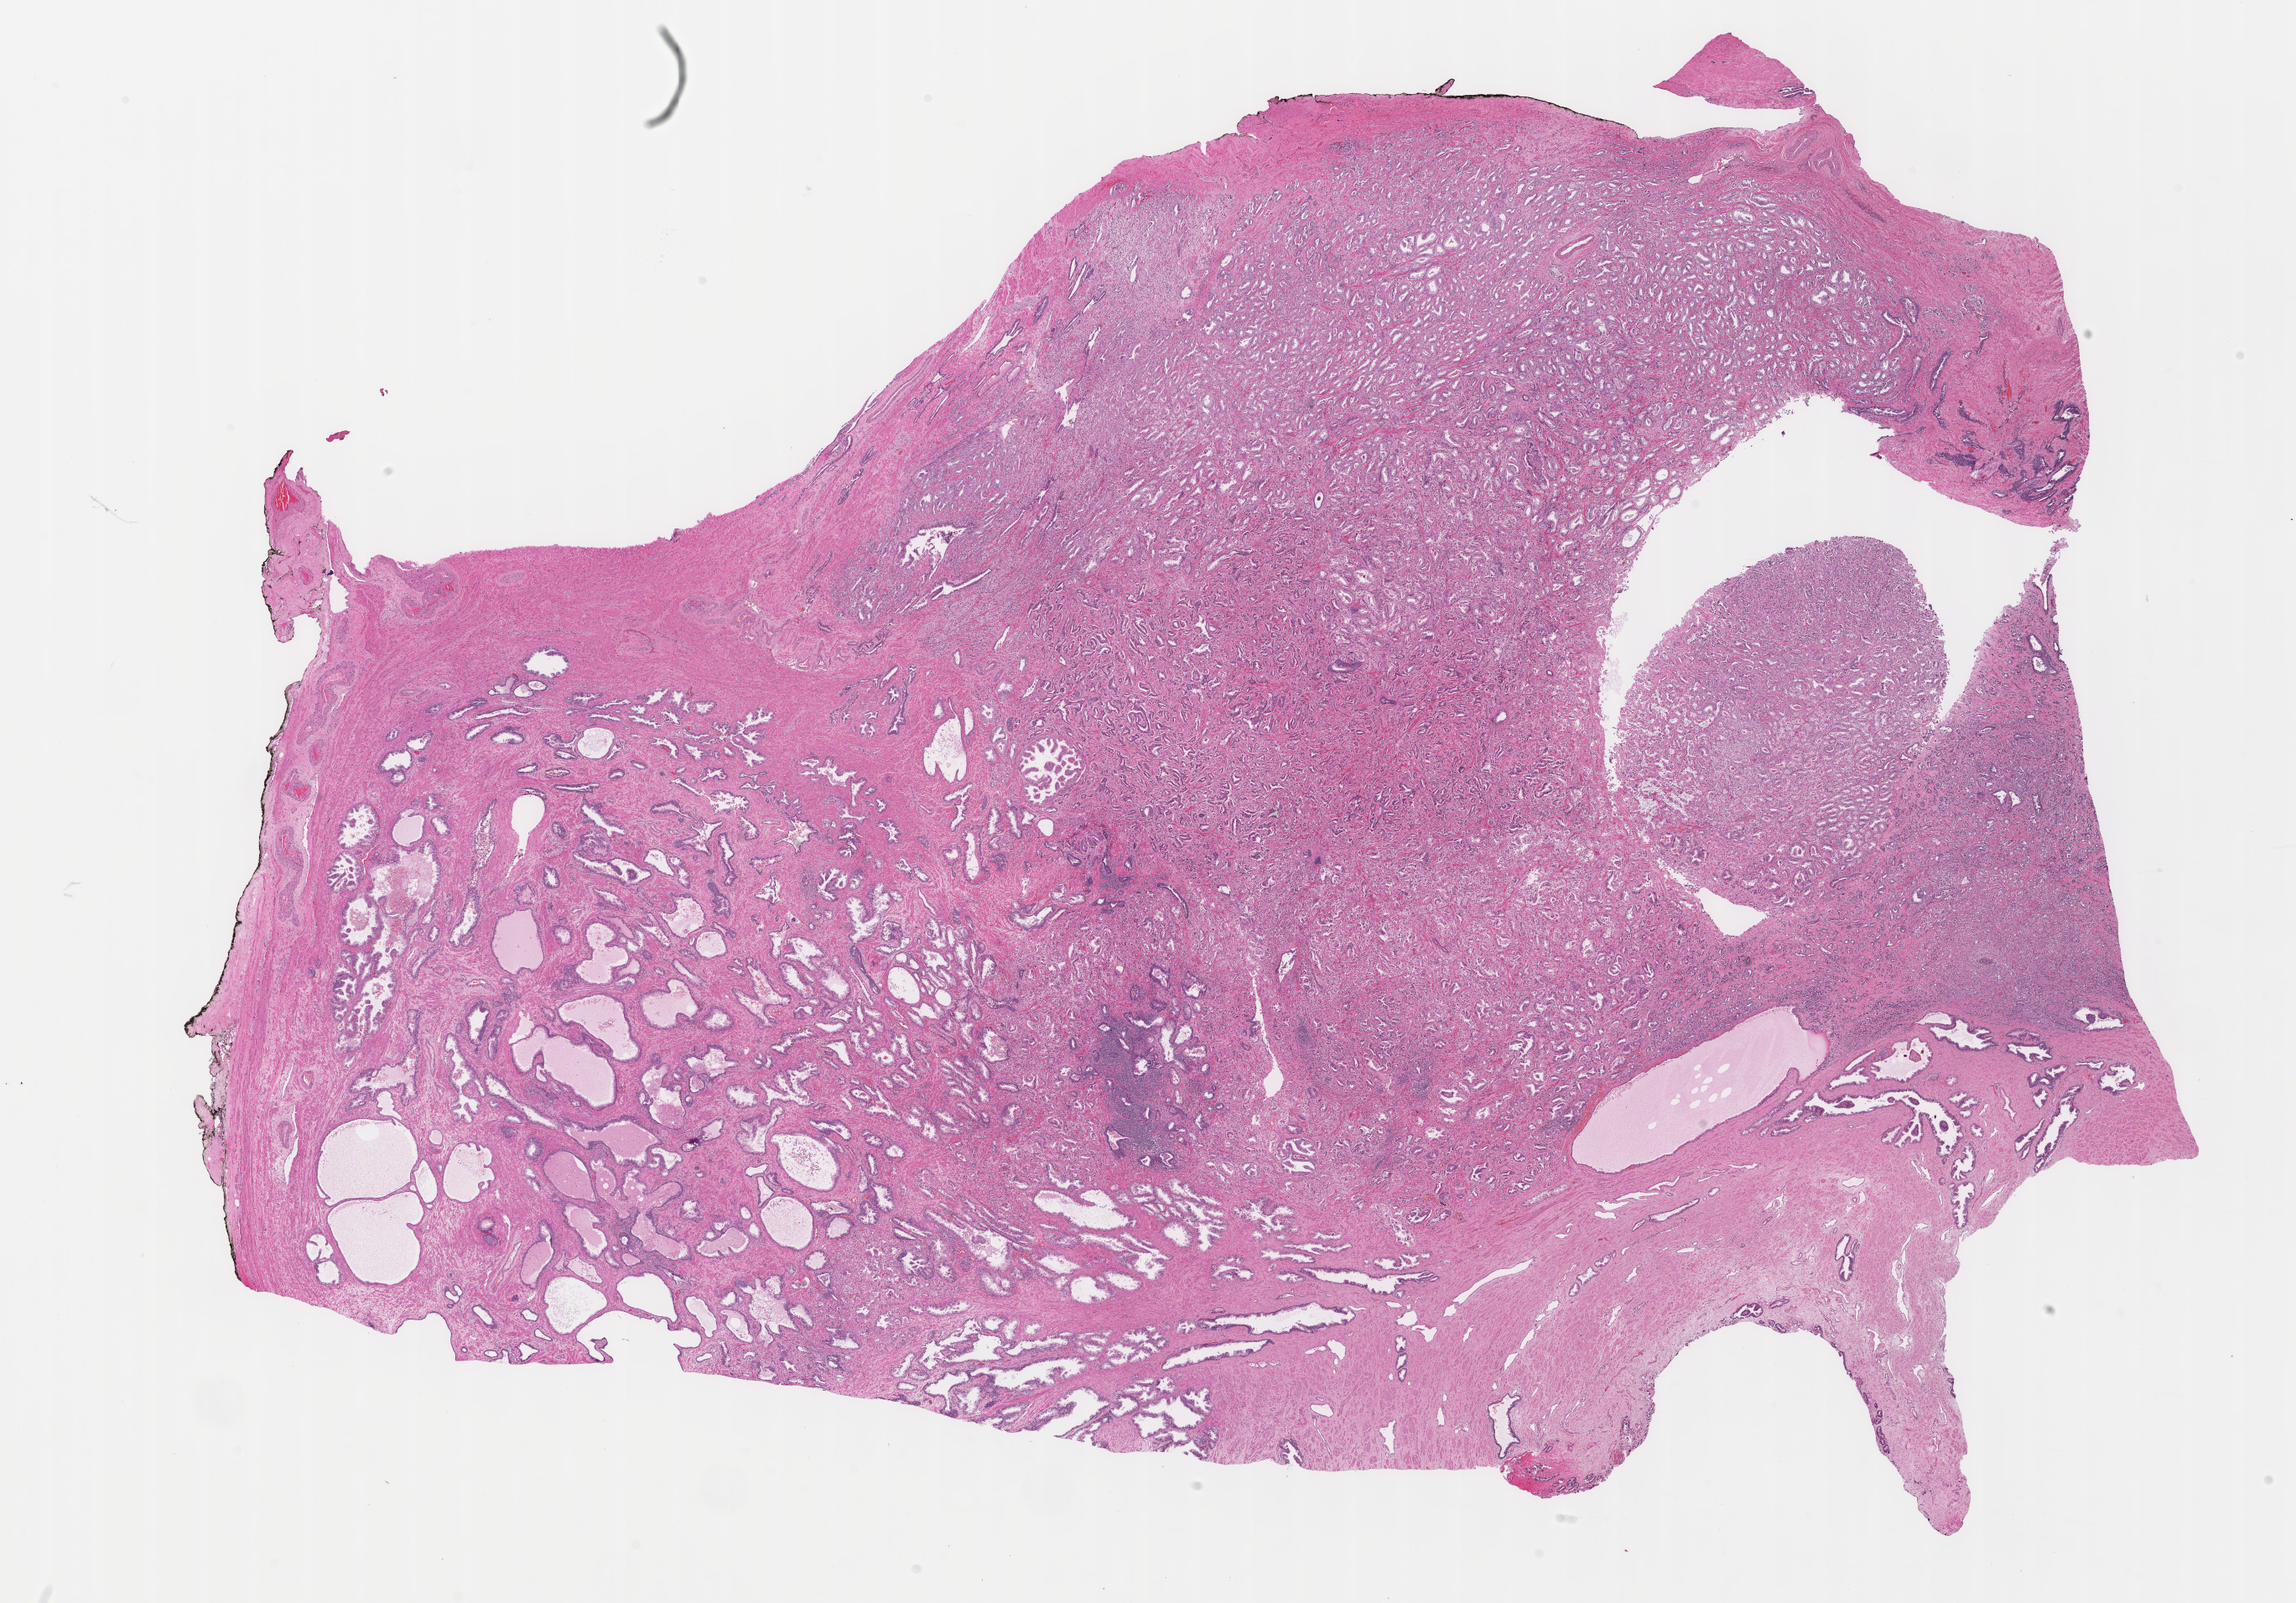
Whole-slide histology image, Hematoxylin and eosin (H&E) stained — shown as a low-resolution overview of the whole scanned area (about 22.1 x 15.5 mm). FFPE section. Primary tumour sample from the prostate. Male patient; age at initial diagnosis 57 years.
Histologic diagnosis: Adenocarcinoma, NOS.